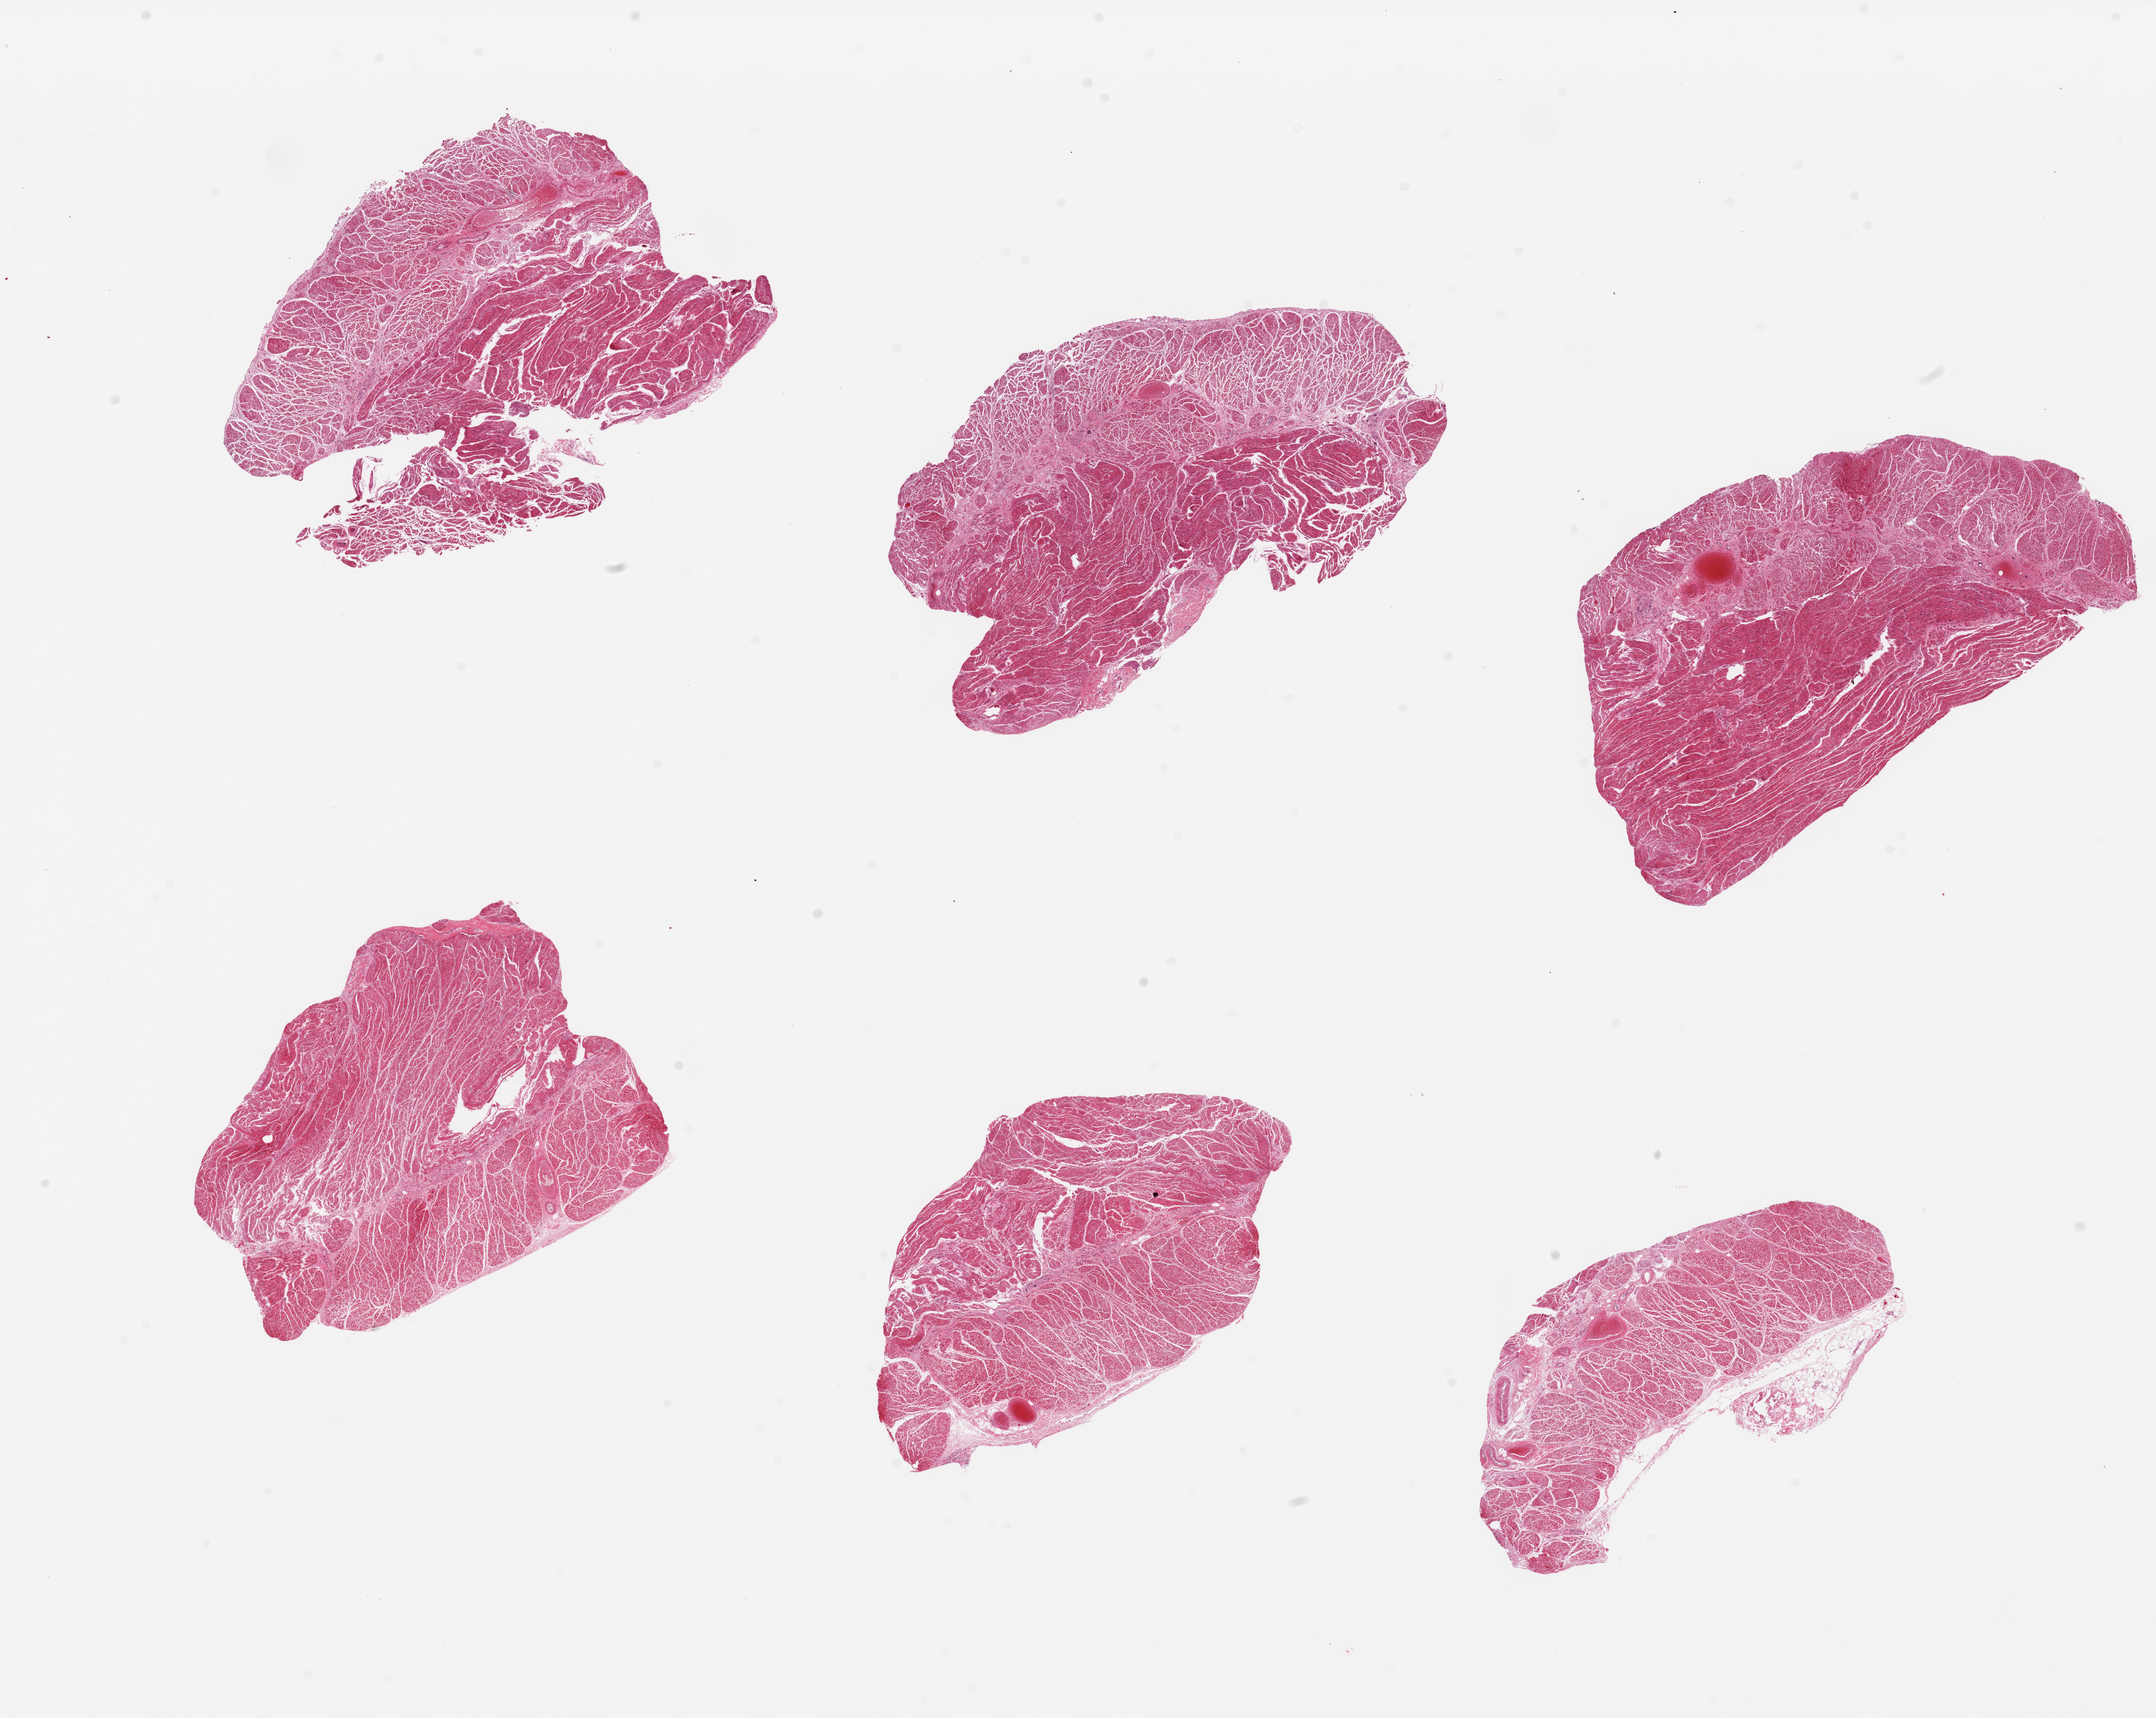
H&E whole-slide image, brightfield — a low-resolution overview of the entire scanned area, about 25.6 x 20.4 mm (from a 20x scan), PAXgene-fixed, paraffin-embedded tissue, sampled site (target tissue): gastroesophageal junction, tissue donor sample. Donor: male.
Reviewer comment on this tissue sample: 6 pieces, all muscularis, good specimen.